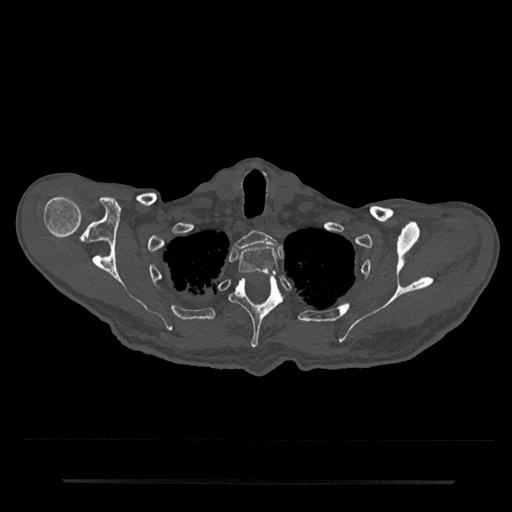
CT including the spine, one axial slice. Position 671 of 797 along the scan axis. Reconstruction kernel Br40s/3. Bone window (W 1800 / L 400 HU). 512 × 512 image matrix, field of view 427 × 427 mm. Patient: male, 74 years. Case-level facts recorded for this patient, not image findings: primary cancer: prostate.
Outlined on this slice (semi-automatic segmentation, software-assisted and operator-edited):
- T1 vertebra: box from (x=235, y=231) to (x=277, y=249) px
- T2 vertebra: (x=238, y=246)–(x=279, y=275)
- T3 vertebra: (x=229, y=275)–(x=283, y=348)